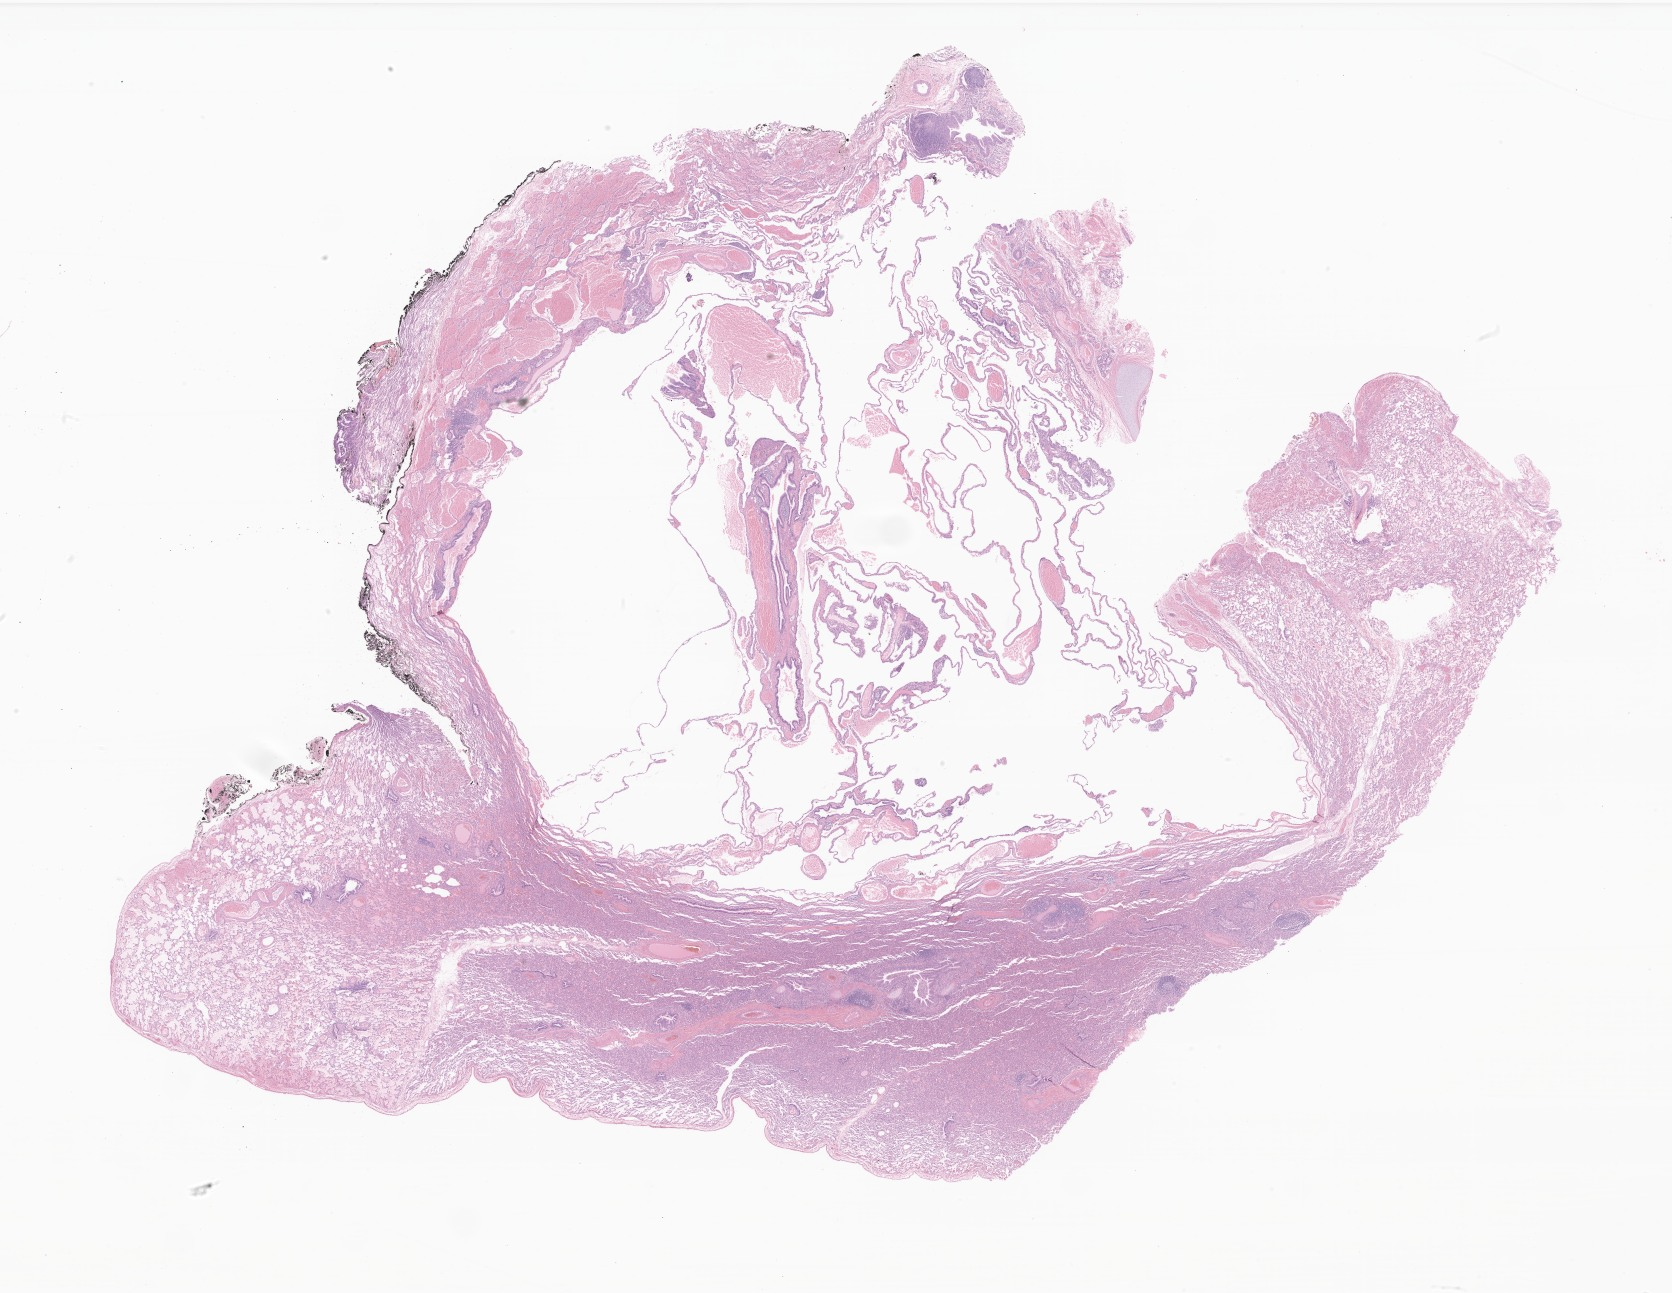
Whole-slide image, haematoxylin and eosin stain of tumor tissue from the upper lobe of lung — shown as a low-resolution overview of the whole scanned area (about 28.2 x 21.8 mm), formalin-fixed, paraffin-embedded (FFPE) tissue. Female patient, age 496 days (about 1.4 years).
Diagnosis (ICD-O-3 morphology term): Pleuropulmonary blastoma.